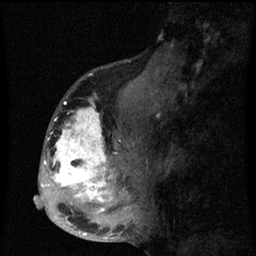
Breast MRI (dynamic contrast-enhanced), one sagittal slice. Slice 29 of 60 in the series (ordered by position). Dynamic contrast-enhanced series, image 2 of 3 at this slice position (ordered by acquisition). 1.5 T. TE 4.2 ms, TR 8 ms. 256 × 256 image matrix. Patient: female, 50 years.
Annotated regions visible in this slice (semi-automatic segmentation, software-assisted and operator-edited):
- analysis volume of interest (the breast-tissue region the enhancement analysis was run in; not a lesion): bounding box <43,90,142,216> (left, top, right, bottom; pixels)
- tumour enhancement mask (voxels above the 70 % enhancement threshold inside the analysis volume of interest): <43,98,116,212>